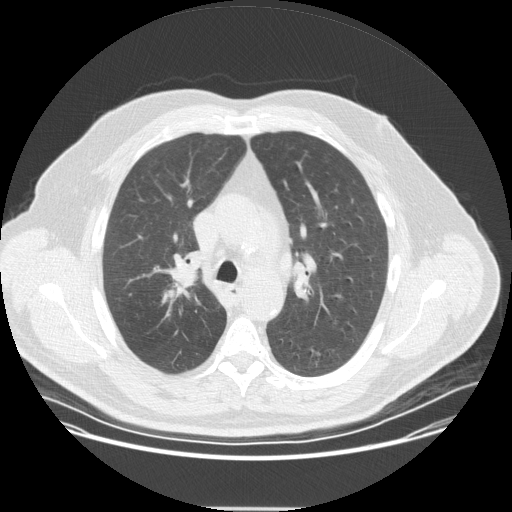
Axial slice from a low-dose chest CT screening exam, second screening round (one year after baseline), lung window (W 1500 / L -600 HU), 2.5 mm slice thickness, 120 kVp, slice 117 of 351 in the series, 512 × 512 image matrix. Male participant, aged 57 years at enrolment. Current smoker at enrolment.
Expert-annotated lung lesion, bounding box <146,250,210,312> (left, top, right, bottom; pixels). Screening reader's record for this exam (one nodule recorded; not confirmed to be the boxed lesion): non-calcified nodule or mass ≥4 mm, right upper lobe, 20 × 16 mm, spiculated (stellate) margins, soft tissue attenuation, pre-existing on the prior screen: no. Official screen result: positive, other. Participant outcome: lung cancer diagnosed 35 days after this screen — non-small cell carcinoma, right upper lobe, poorly differentiated (G3), stage IIA (AJCC 6th edition), 25 mm at pathology.